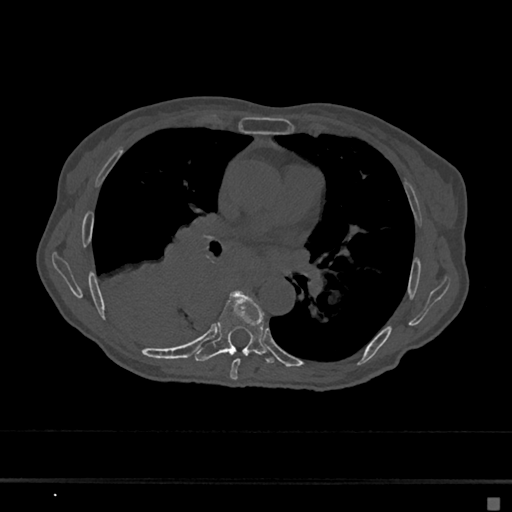
CT including the spine, one axial slice; slice 388 of 797 in the series (ordered by position); reconstruction kernel Br40s/3; 120 kVp; bone window (W 1800 / L 400 HU); 0.5 mm slice thickness; 512 × 512 image matrix, field of view 360 × 360 mm. Patient: female, 68 years. Case-level facts recorded for this patient, not image findings: primary cancer: renal.
Structures marked on this image (semi-automatically segmented with operator editing):
- T6 vertebra: bounding box <229,359,240,380> (left, top, right, bottom; pixels)
- T7 vertebra: <195,291,275,365>